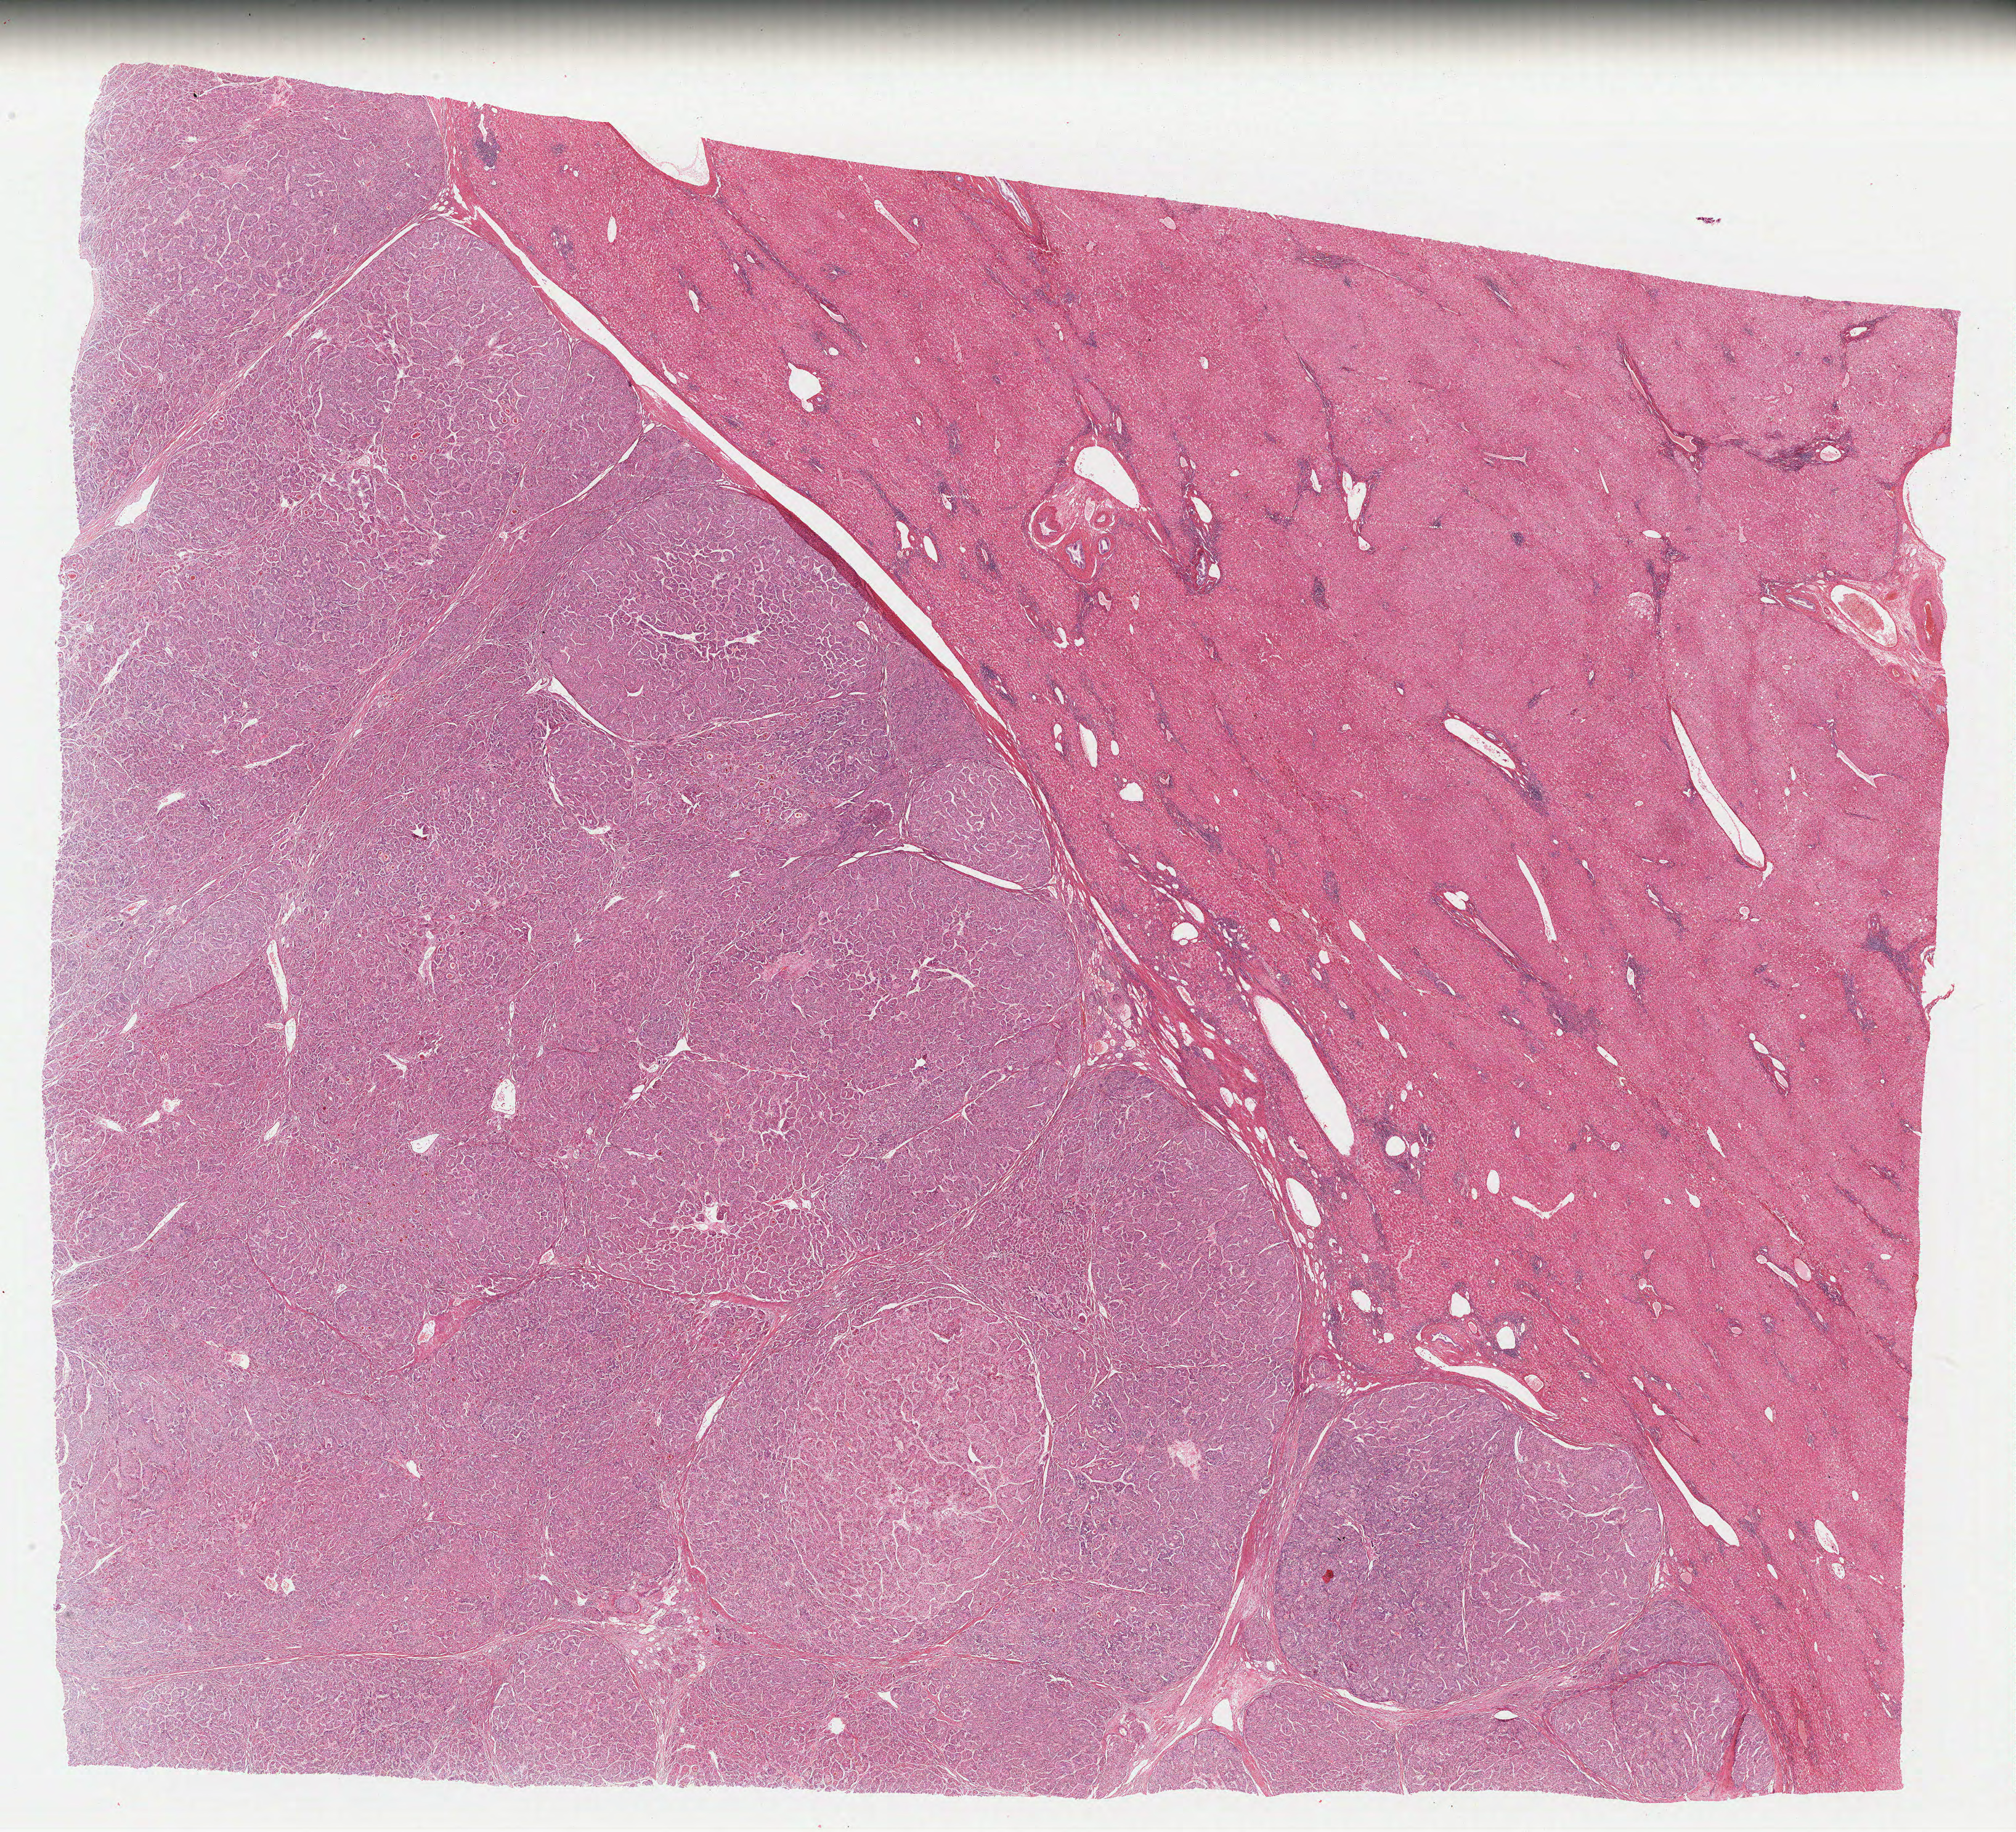
Digitized H&E tissue section (whole slide), low-resolution overview of the scanned area, about 25.9 x 23.5 mm (from a 40x scan); formalin-fixed paraffin-embedded (FFPE) diagnostic section; liver, primary tumour sample. Patient: male, age at initial diagnosis 56 years. Histologic grade: G2 (moderately differentiated).
Diagnosis: Hepatocellular carcinoma, NOS. AJCC pathologic stage: I.